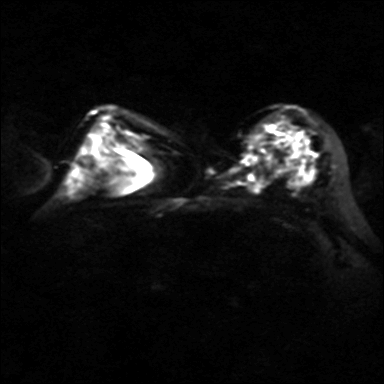
Breast MRI, one axial slice; slice 25 of 40 in the series (ordered by position); diffusion-weighted series; image 2 of 4 stored at this slice position (different b-values; order by instance number); 3 T; 384 × 384 image matrix, field of view 320 × 320 mm. Female patient.
Annotated regions visible in this slice (outlined manually by an expert reader):
- tumour on diffusion-weighted imaging: bounding box (x1, y1, x2, y2) in pixels: (248, 129, 306, 183)